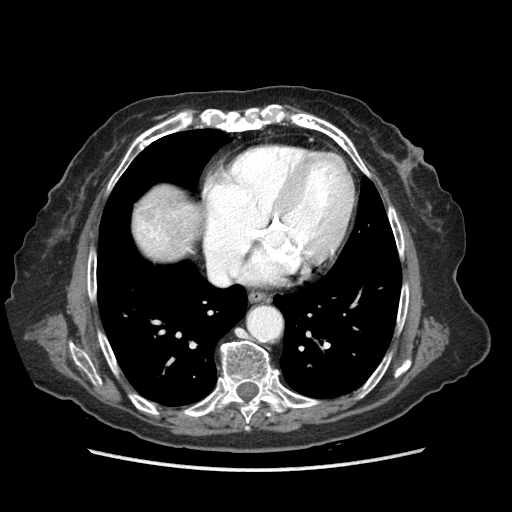
Contrast-enhanced abdominal CT (liver protocol), one axial slice; slice 81 of 89 in the series (ordered by position); reconstruction kernel STANDARD; 140 kVp; soft-tissue window (W 400 / L 40 HU); 2.5 mm slice thickness; 512 × 512 image matrix. From the clinical record (not read from this slice): diagnosis: hepatocellular carcinoma (patient treated with transarterial chemoembolisation; whether this scan precedes or follows treatment is not stated here); TNM stage (as recorded): Stage-IIIA; Child-Pugh class: A; tumour differentiation: well differentiated; tumour size: 11 cm.
Outlined on this slice (semi-automatic segmentation, software-assisted and operator-edited):
- liver parenchyma outside the tumour (the mass and vessels are separate outlines, so this box may not span the whole liver): box from (x=134, y=184) to (x=198, y=260) px
- liver vessels: (x=142, y=223)–(x=160, y=241)